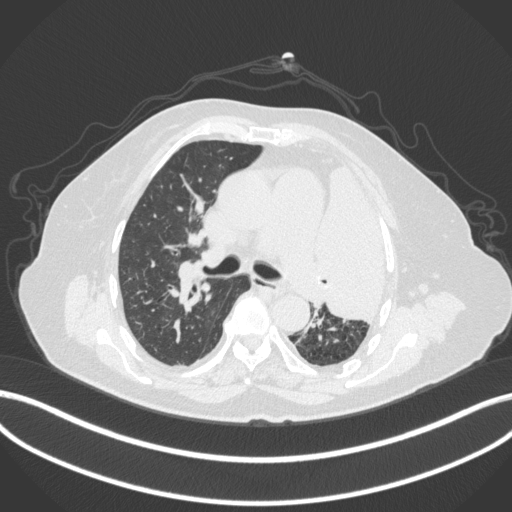
Chest CT, one axial slice. Slice 244 of 399 in the series (ordered by position). Lung window (W 1500 / L -600 HU). 1 mm slice thickness. 512 × 512 image matrix, field of view 400 × 400 mm. Female patient, age 75 years. Case-level facts recorded for this patient, not image findings: clinical TNM (as recorded): T3 N3 M1.
Outlined on this slice (bounding box drawn by a radiologist):
- lung tumour (recorded histology: adenocarcinoma): bounding box <316,161,391,325> (left, top, right, bottom; pixels)